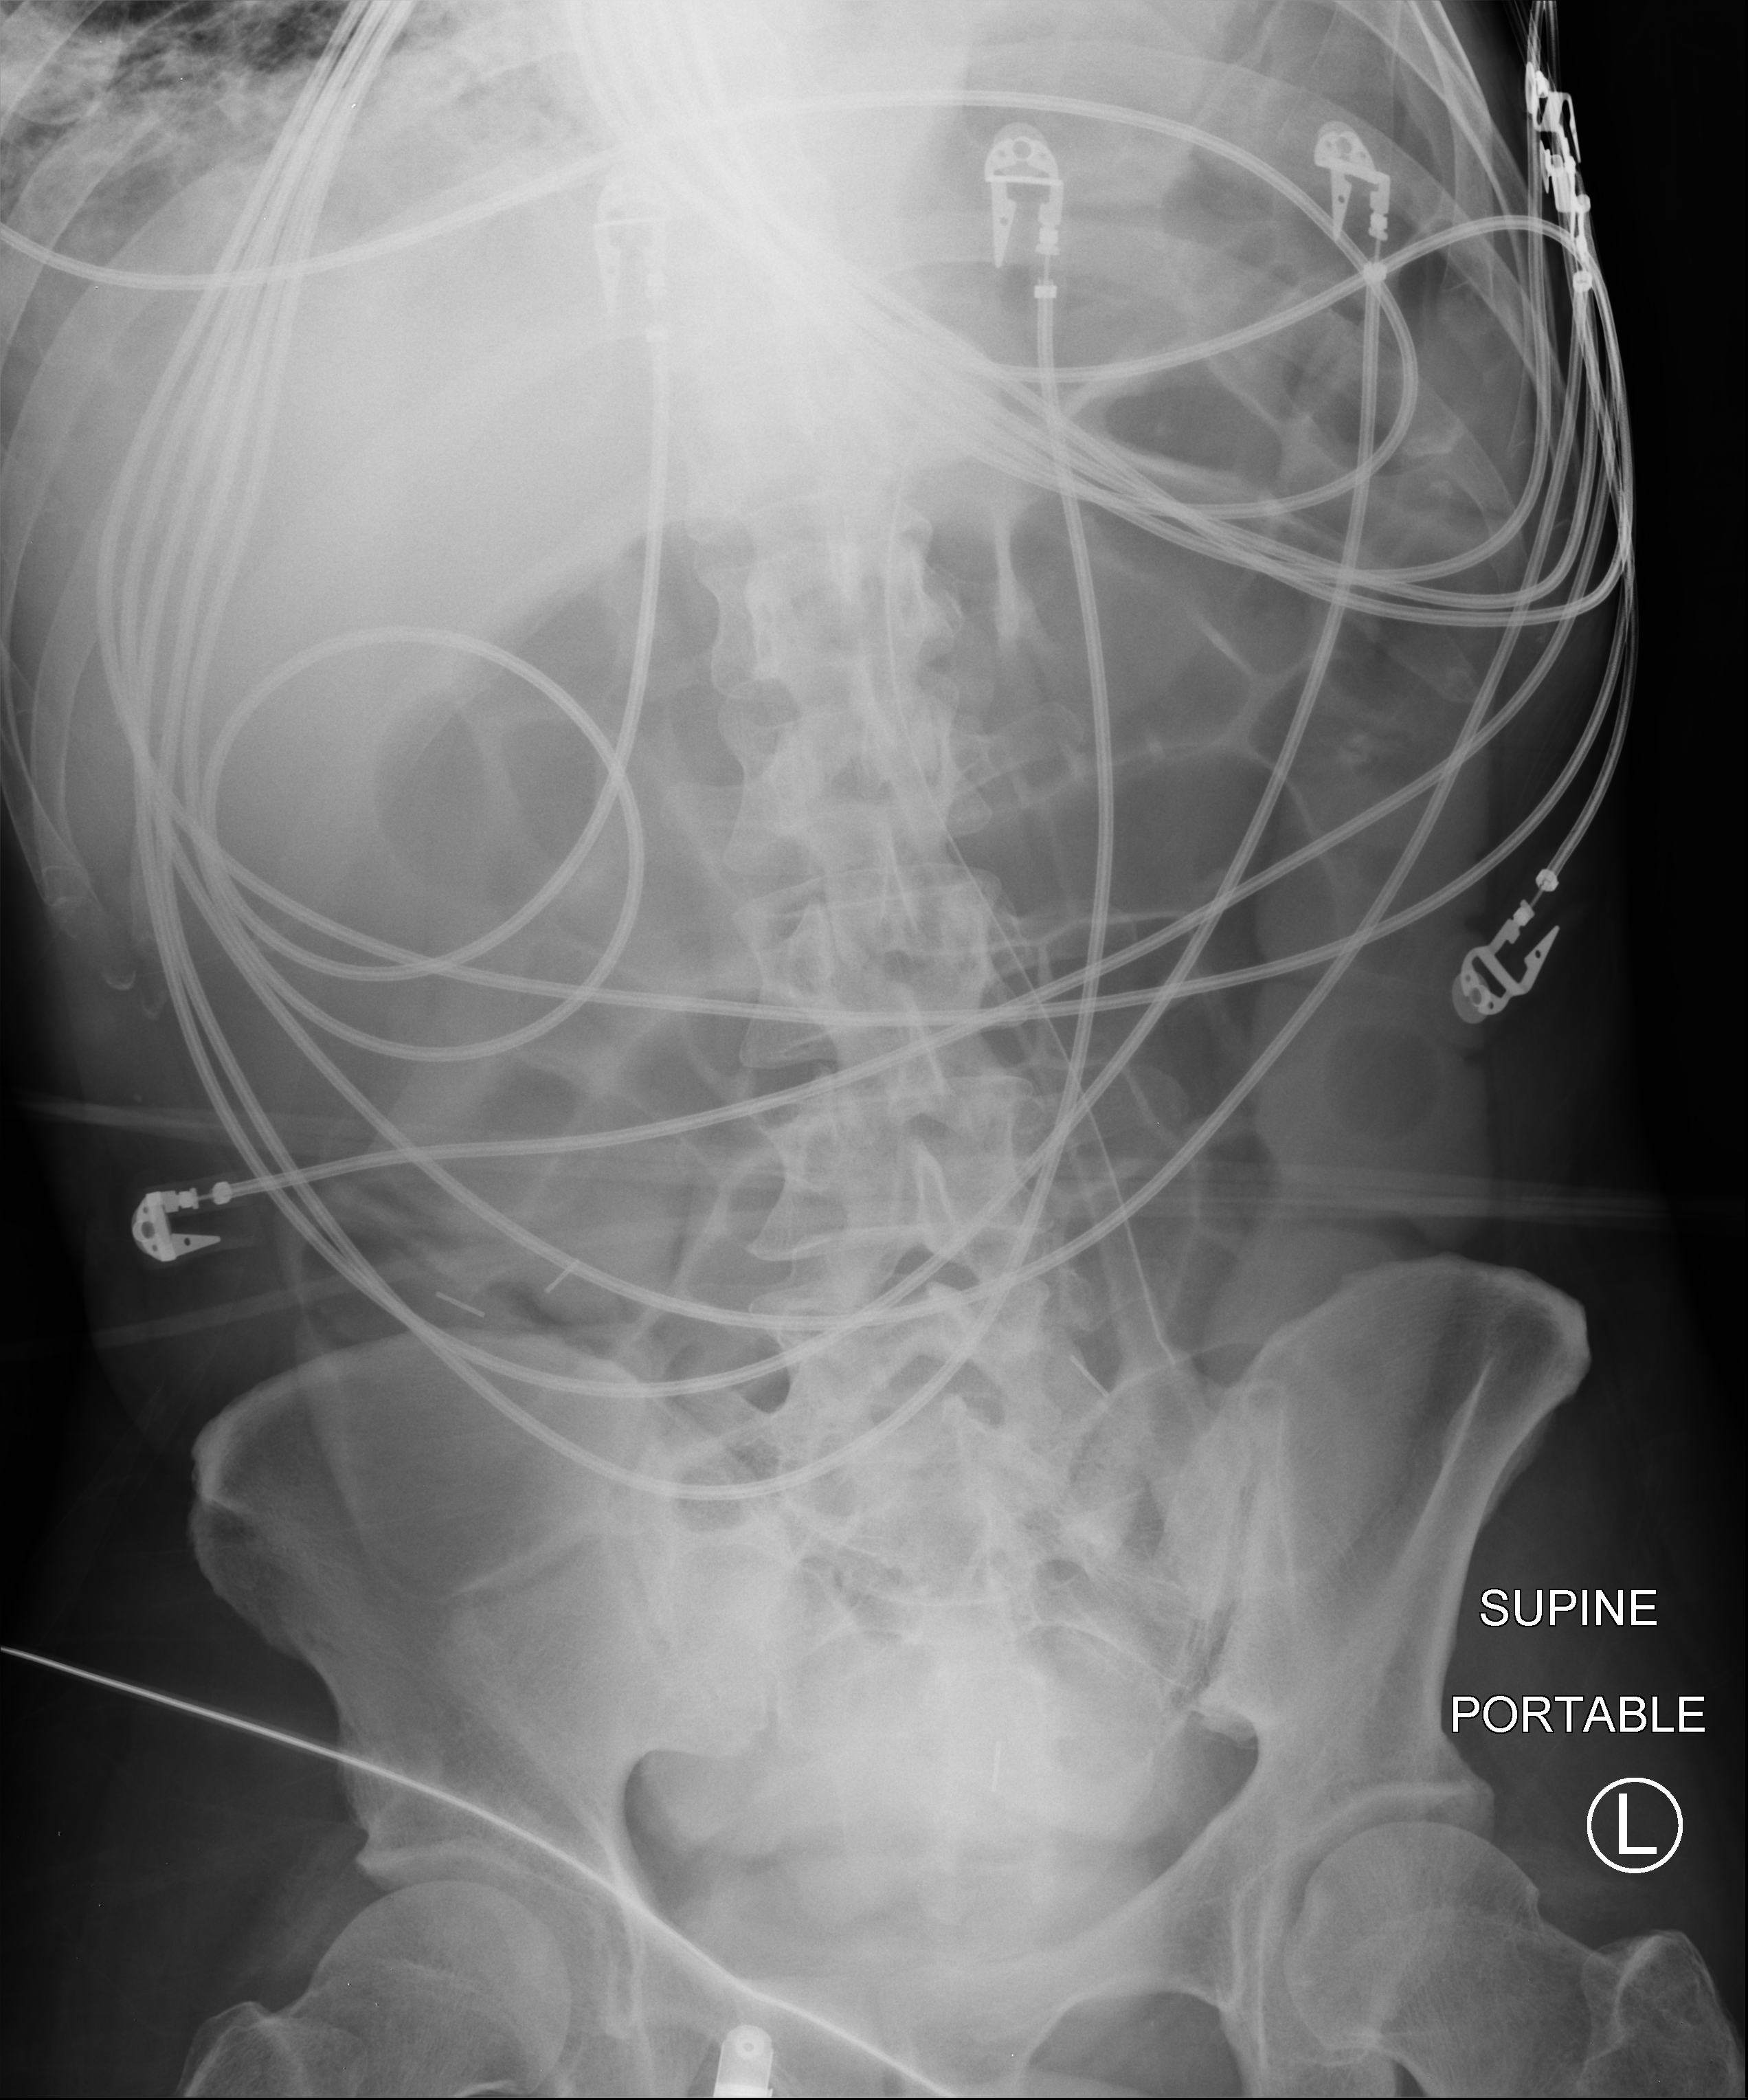
Abdomen X-ray (portable), anteroposterior (AP) projection. Male patient hospitalised with COVID-19, age 18–59 years.
Hospital-stay facts (about this admission, not read from this image; timing relative to this image not recorded): mechanically ventilated during this hospital stay: yes.